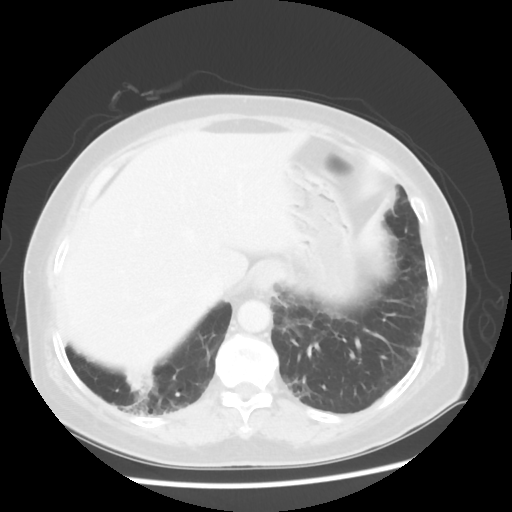
Chest CT, one axial slice; position 12 of 56 along the scan axis; lung window (W 1500 / L -600 HU); 5 mm slice thickness; 512 × 512 image matrix, field of view 360 × 360 mm. Female patient, age 64 years. Case-level facts recorded for this patient, not image findings: clinical TNM (as recorded): Tis N0 M0.
Outlined on this slice (rectangle marked by the reading radiologist):
- lung tumour (recorded histology: adenocarcinoma): bounding box (x1, y1, x2, y2) in pixels: (118, 361, 172, 427)